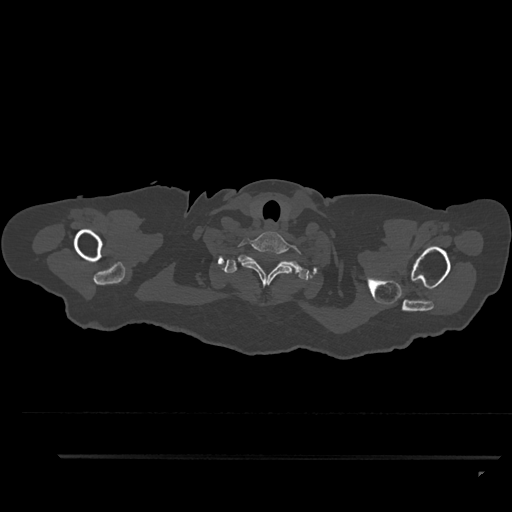
CT including the spine, one axial slice; reconstruction kernel Br40s/3; 120 kVp; bone window (W 1800 / L 400 HU); 512 × 512 image matrix. Patient: female, 44 years. Case-level facts recorded for this patient, not image findings: primary cancer: renal; vertebrae with lytic lesions (as recorded): L1.
Outlined on this slice (semi-automatic segmentation, software-assisted and operator-edited):
- T1 vertebra: bounding box (x1, y1, x2, y2) in pixels: (222, 255, 309, 281)